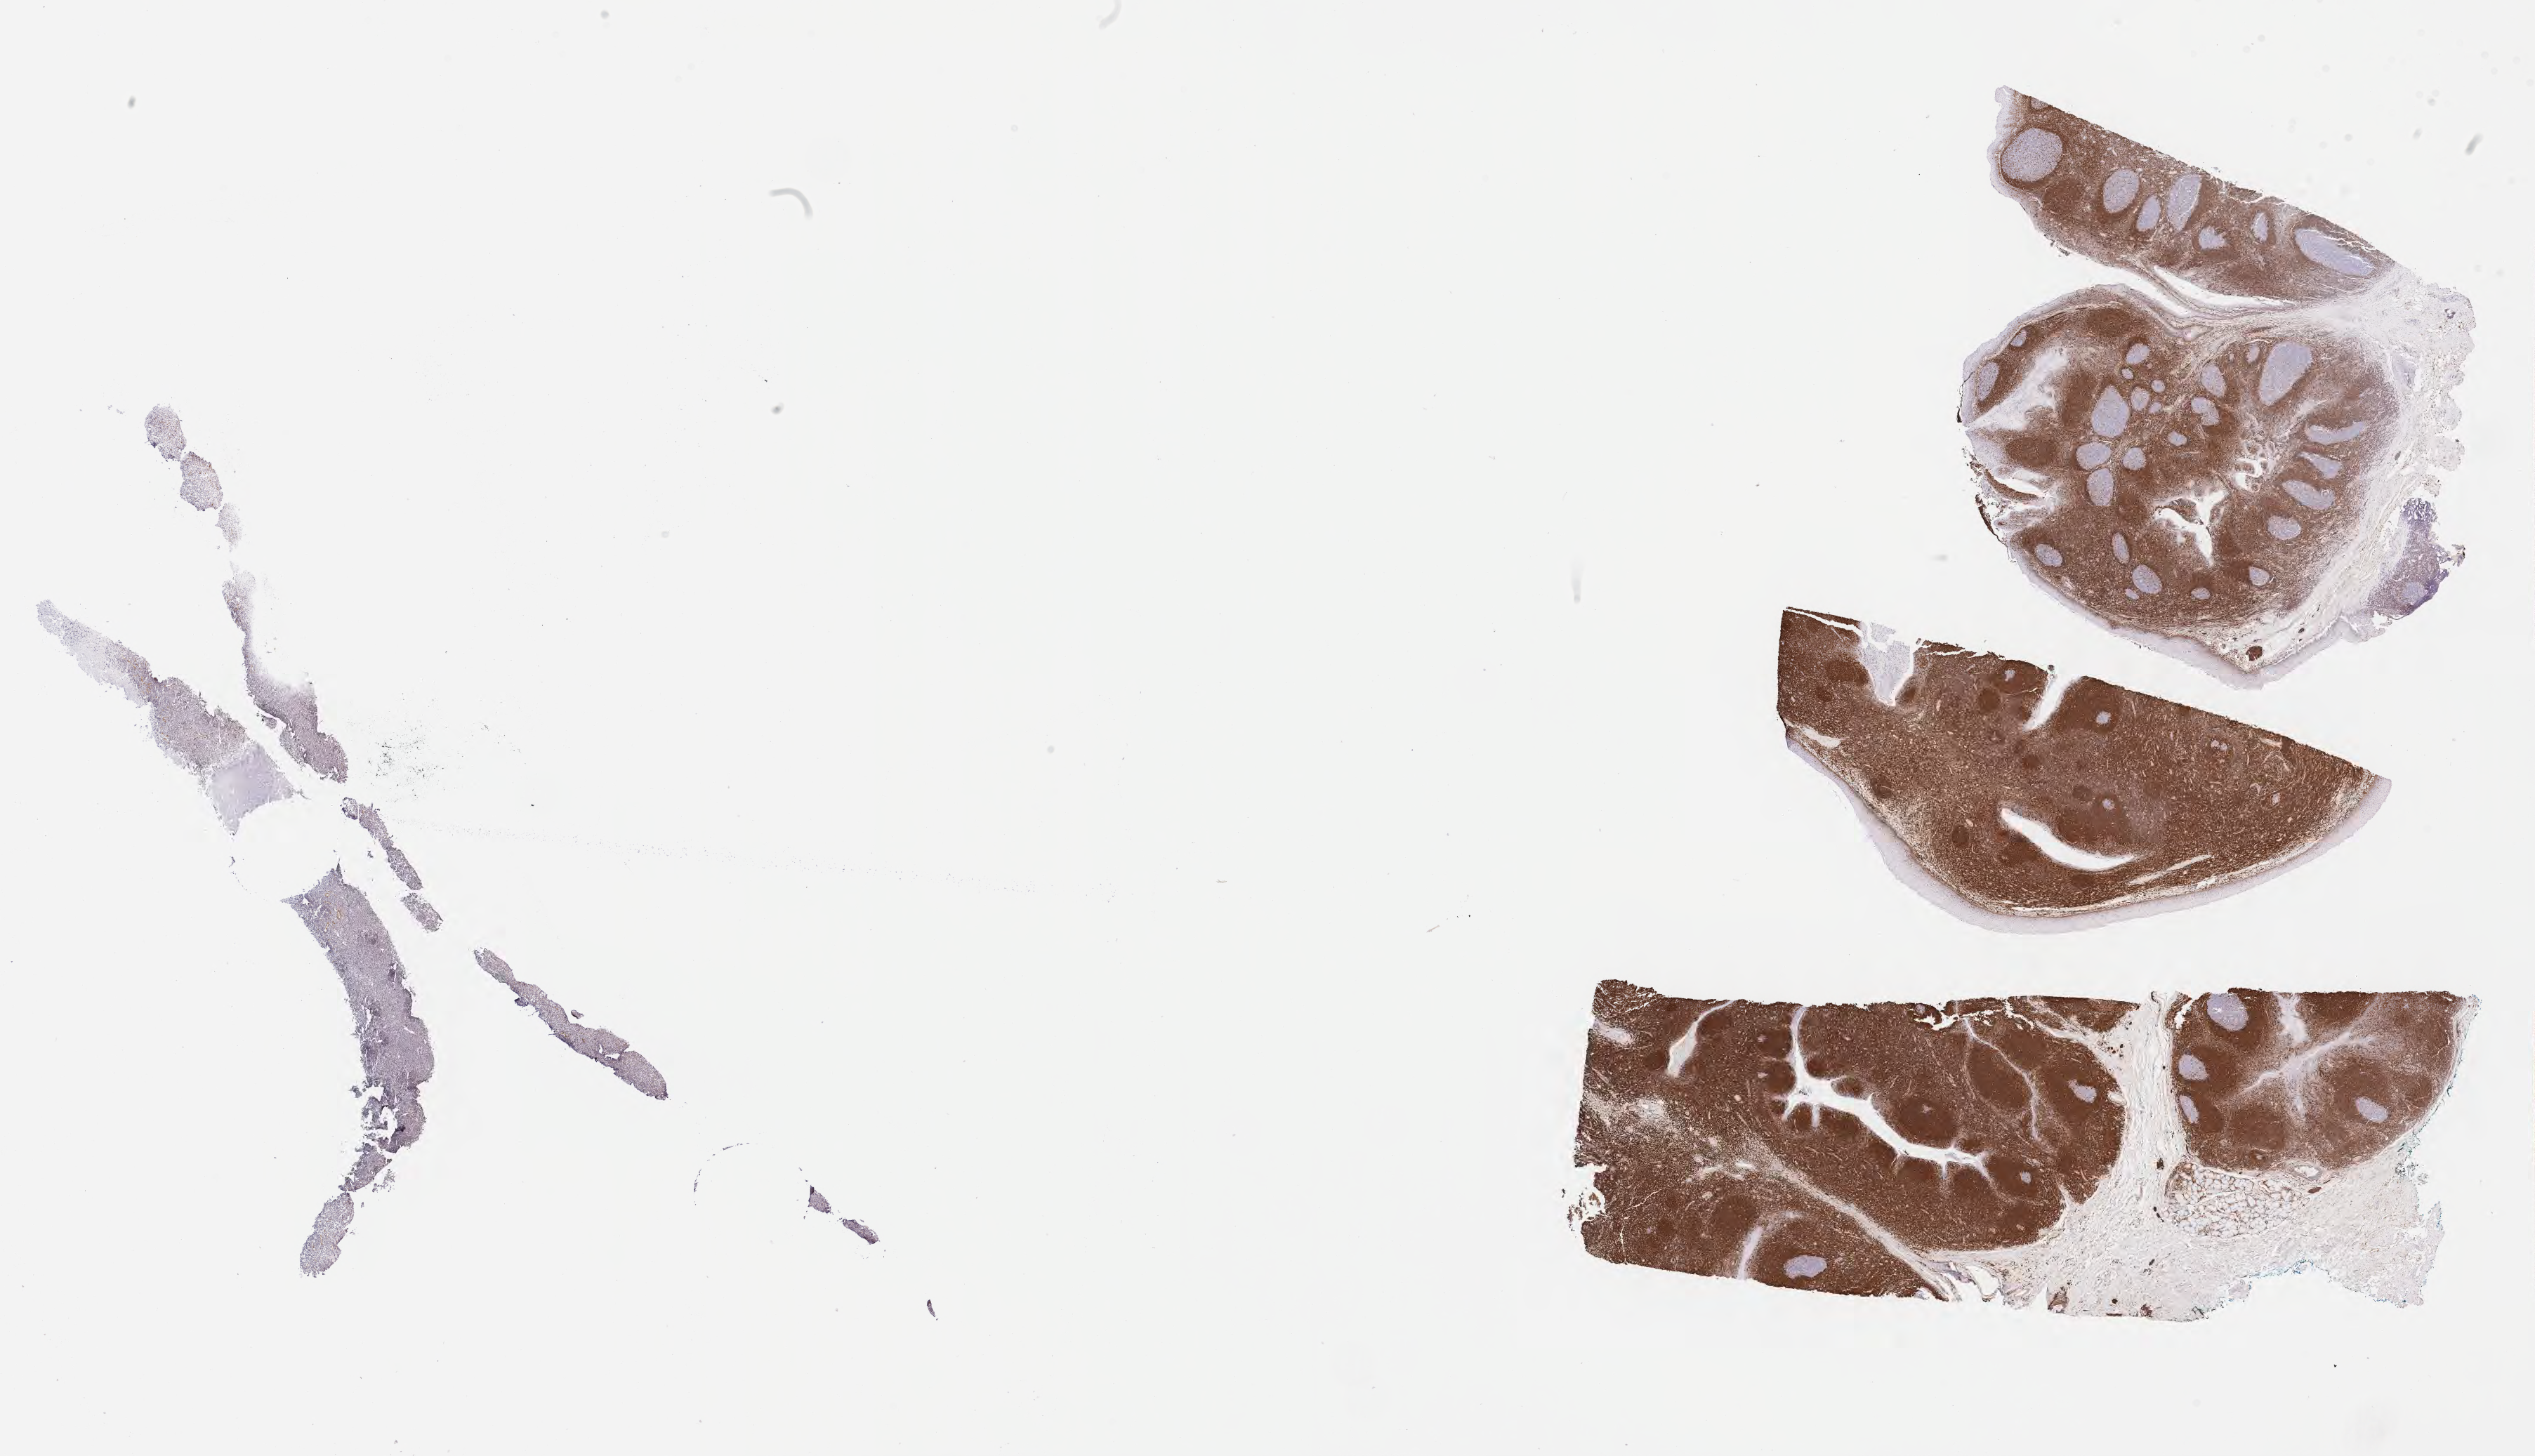
IHC for BCL2, whole-slide image — whole scanned area (about 29.2 x 16.8 mm) shown as a low-resolution overview; specimen: tumor tissue; site: abdomen proper. Male patient, age 14 years.
Diagnosis: Burkitt lymphoma, NOS.